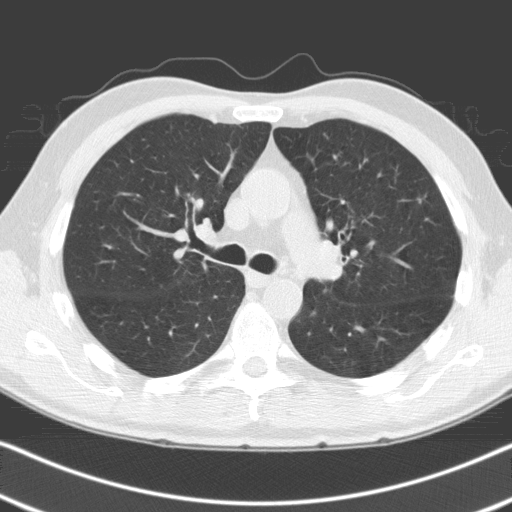
Axial slice from a low-dose chest CT screening exam; second annual screen; lung window (W 1500 / L -600 HU); 3.2 mm slice thickness; slice 61 of 163 in the series. Male, age 68 years at enrolment. Former smoker at enrolment.
Expert reader's lesion annotation, bounding box <395,182,442,223> (left, top, right, bottom; pixels). No non-calcified nodule or mass ≥4 mm was recorded by the screening reader at this exam. Participant outcome: lung cancer diagnosed 685 days after this screen (after the third annual screen) — adenocarcinoma, NOS, left upper lobe, moderately differentiated (G2), stage IA (AJCC 6th edition), 6 mm at pathology.